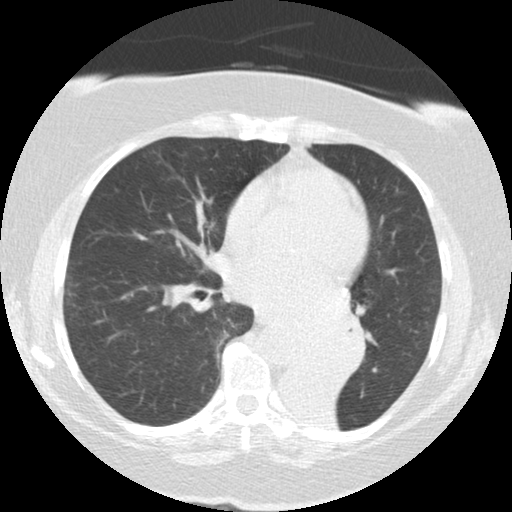
Axial slice from a low-dose chest CT screening exam. First (baseline) screen. Lung window (W 1500 / L -600 HU). 2.5 mm slice thickness. 120 kVp. Female, age 71 years at enrolment.
Expert reader's lesion annotation, box from (x=284, y=305) to (x=366, y=383) px. Reader record for this screening exam (exam-level; its link to the box is not recorded): non-calcified nodule or mass ≥4 mm, right middle lobe, 5 × 5 mm, smooth margins, soft tissue attenuation. Note: the box lies in the patient's left hemithorax on this image, whereas the reader's record names the right lung; they may be different findings. Lung cancer was diagnosed 46 days after this screen: large cell carcinoma, NOS, left lower lobe, mediastinum, other location, poorly differentiated (G3), stage IV (AJCC 6th edition), 50 mm at pathology.